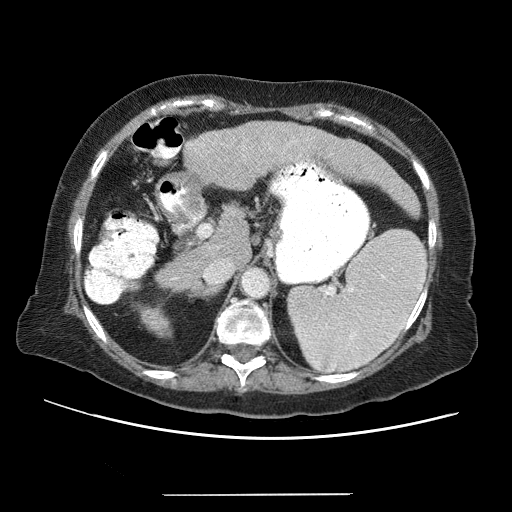
Contrast-enhanced abdominal CT (liver protocol), one axial slice; position 35 of 65 along the scan axis; 120 kVp; soft-tissue window (W 400 / L 40 HU); 512 × 512 image matrix, field of view 380 × 380 mm. Case-level facts recorded for this patient, not image findings: diagnosis: hepatocellular carcinoma (patient treated with transarterial chemoembolisation; whether this scan precedes or follows treatment is not stated here); TNM stage (as recorded): Stage-IIIB; Child-Pugh class: A.
Outlined on this slice (semi-automatically segmented with operator editing):
- liver parenchyma outside the tumour (the mass and vessels are separate outlines, so this box may not span the whole liver): box from (x=123, y=122) to (x=420, y=338) px
- liver vessels: (x=136, y=139)–(x=366, y=328)